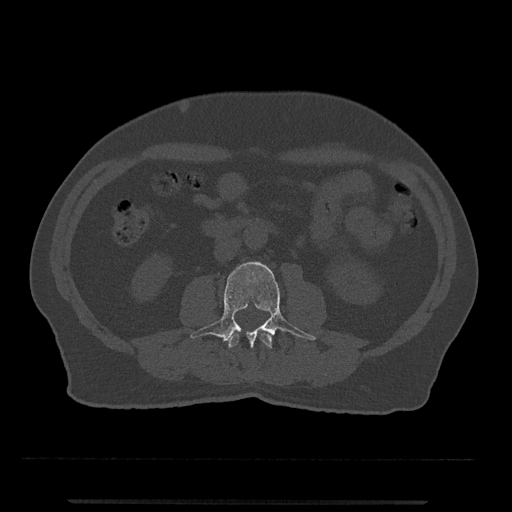
CT including the spine, one axial slice. 120 kVp. Bone window (W 1800 / L 400 HU). 0.5 mm slice thickness. 512 × 512 image matrix, field of view 419 × 419 mm. Male patient, age 63 years. Case-level facts recorded for this patient, not image findings: primary cancer: prostate.
Annotated regions visible in this slice (semi-automatically segmented with operator editing):
- L2 vertebra: bounding box [x1, y1, x2, y2] px = [227, 333, 272, 350]
- L3 vertebra: [190, 262, 316, 348]